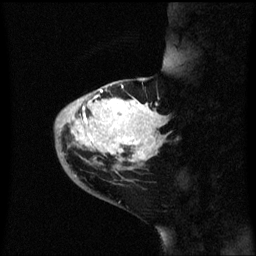
Breast MRI (dynamic contrast-enhanced), one sagittal slice. Slice 18 of 60 in the series (ordered by position). Dynamic contrast-enhanced series, image 2 of 3 at this slice position (ordered by acquisition). 1.5 T. TE 4.2 ms, TR 8.4 ms. 256 × 256 image matrix. Female patient, age 46 years. Case-level facts recorded for this patient, not image findings: setting: breast cancer imaged before/during neoadjuvant chemotherapy; receptor status: HER2-positive.
Outlined on this slice (semi-automatic segmentation, software-assisted and operator-edited):
- analysis volume of interest (the breast-tissue region the enhancement analysis was run in; not a lesion): bounding box <54,86,167,171> (left, top, right, bottom; pixels)
- tumour enhancement mask (voxels above the 70 % enhancement threshold inside the analysis volume of interest): <68,90,163,163>